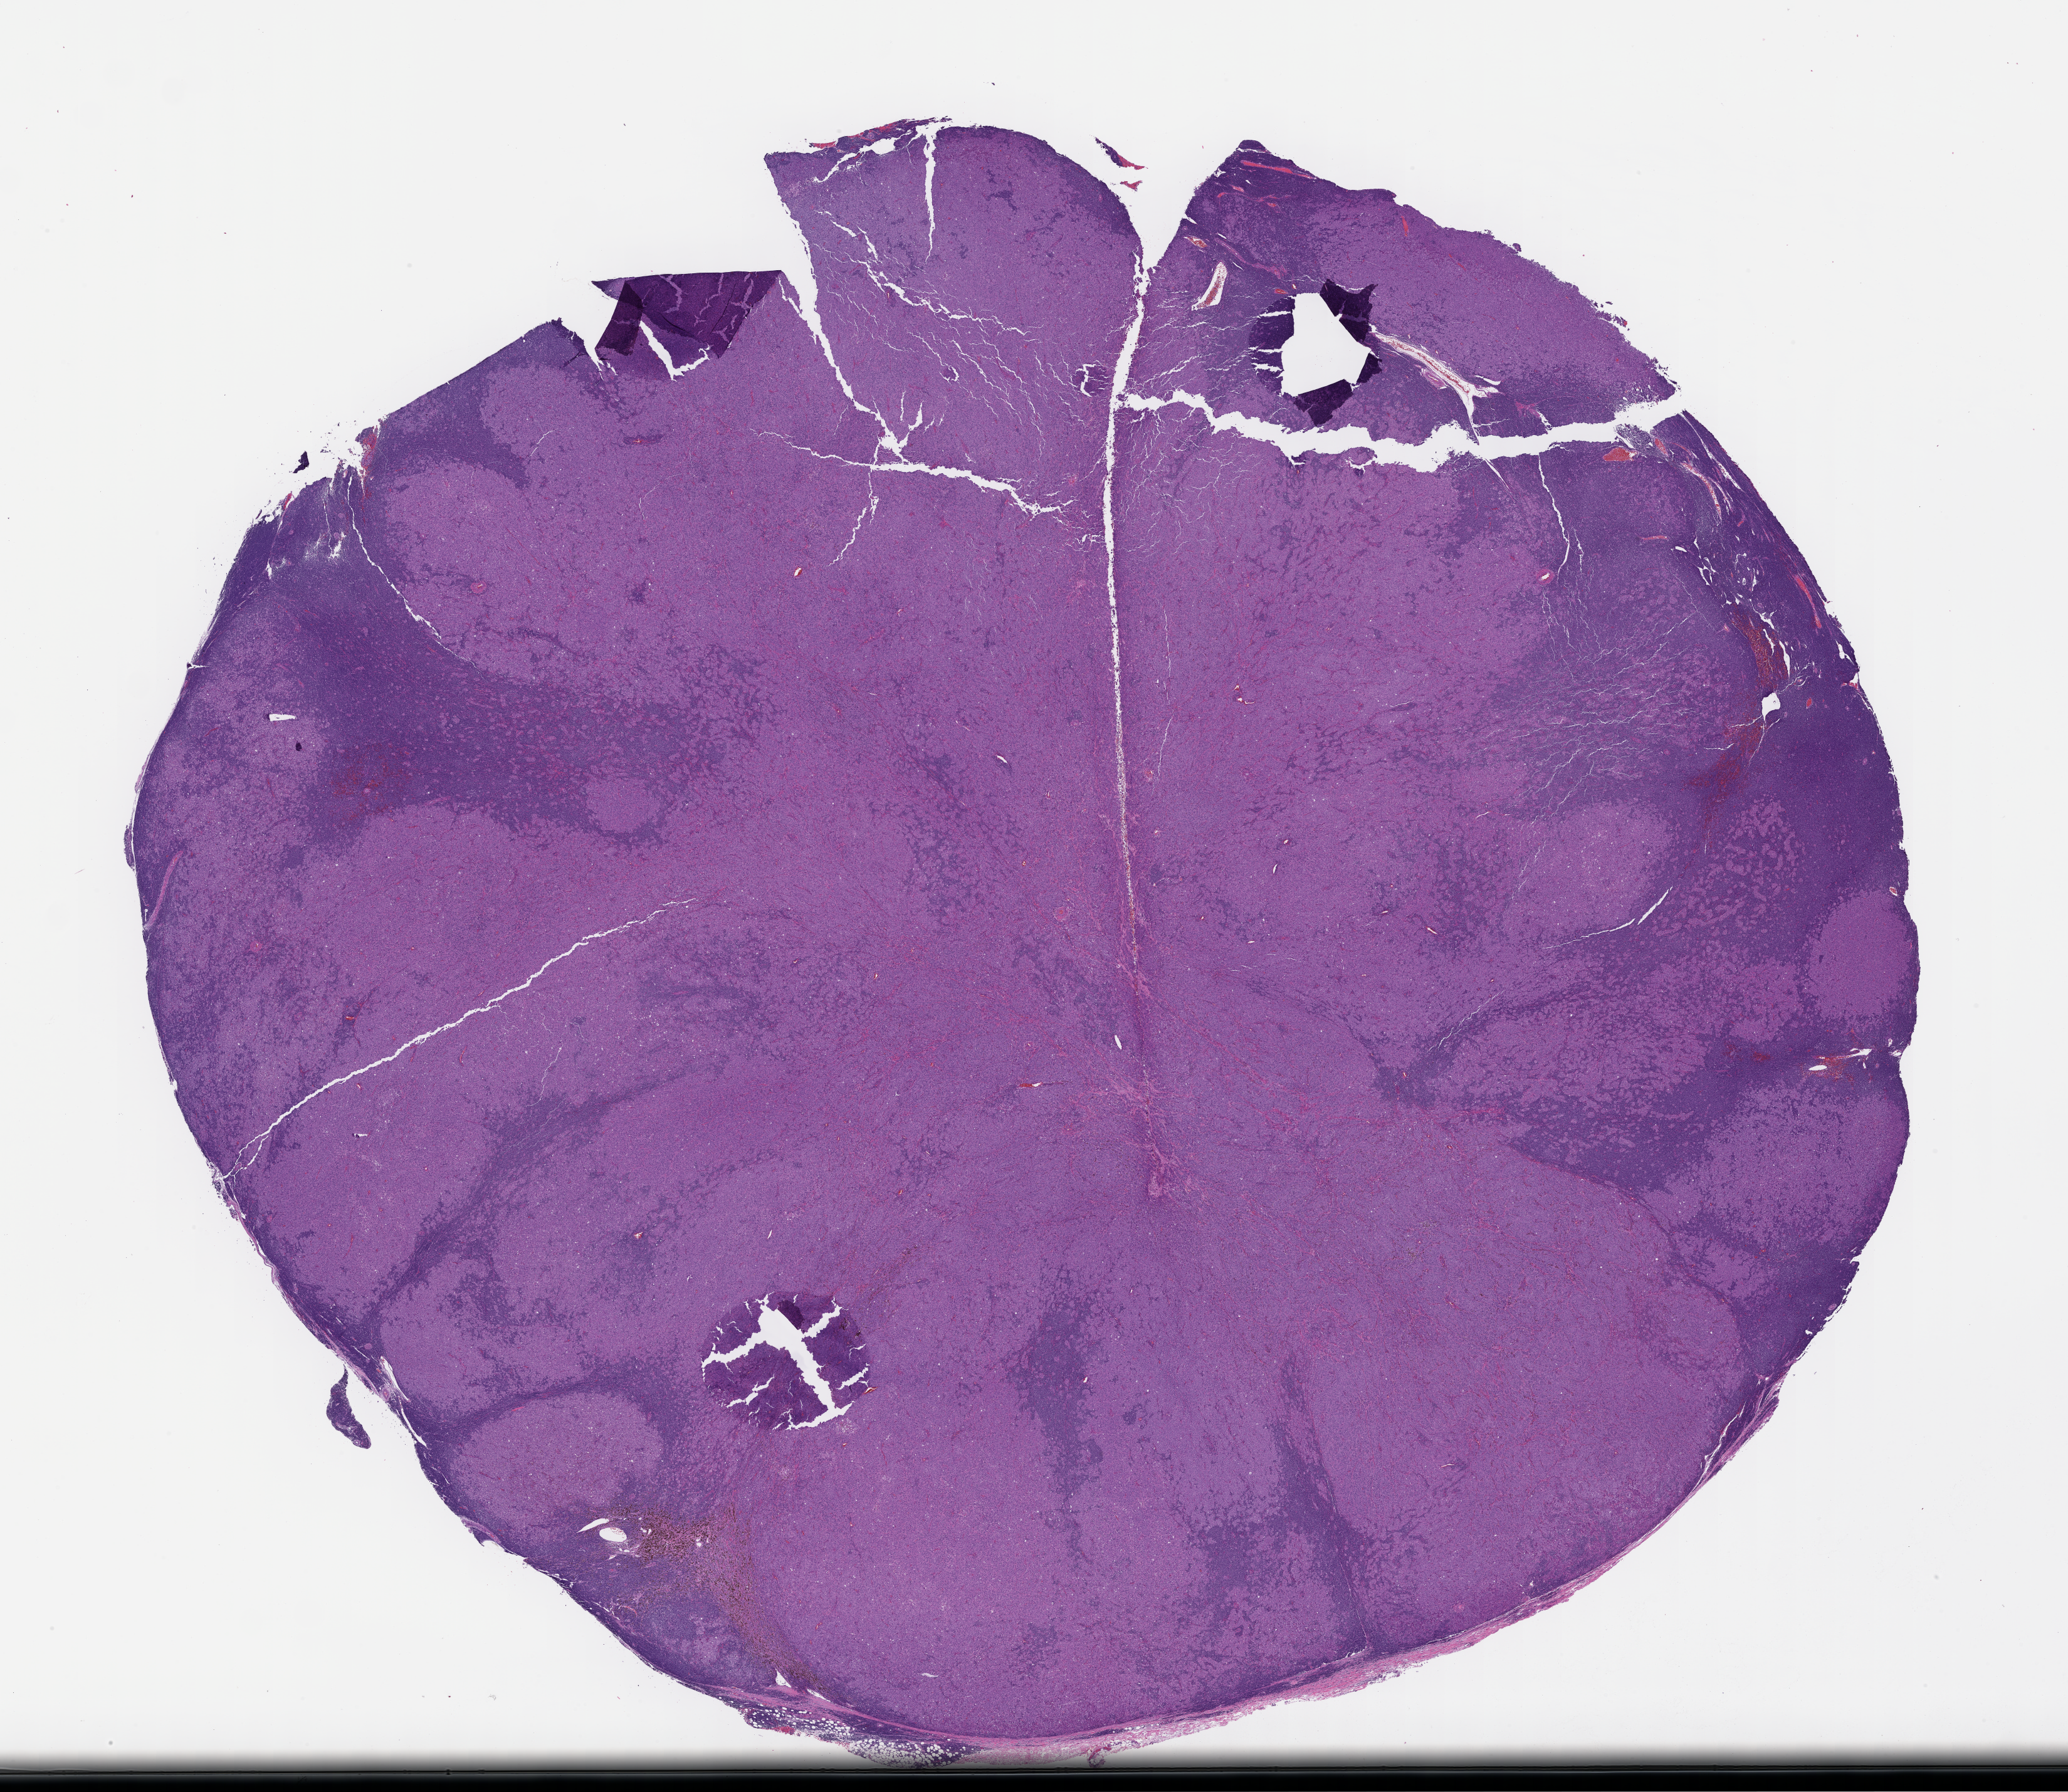
Digitized H&E-stained section, whole scanned area (about 26.6 x 23.1 mm) shown as a low-resolution overview. FFPE section. Archival tissue. Patient sex: male.
This section: metastasis (sampled organ not recorded). Primary diagnosis of the patient: Melanoma.